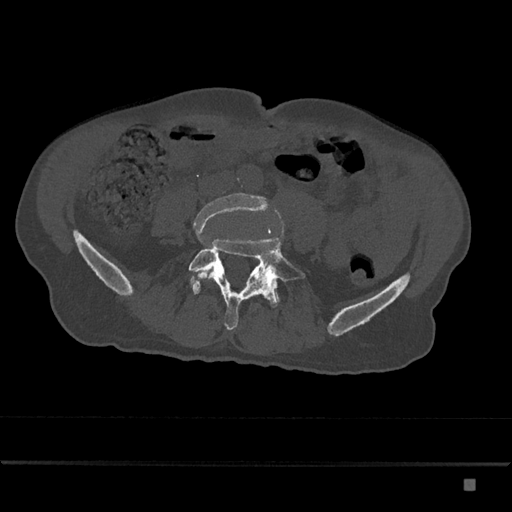
CT including the spine, one axial slice. Position 293 of 797 along the scan axis. 120 kVp. Bone window (W 1800 / L 400 HU). 0.5 mm slice thickness. 512 × 512 image matrix, field of view 390 × 390 mm. Patient: male, 72 years. From the clinical record (not read from this slice): primary cancer: prostate.
Outlined on this slice (semi-automatically segmented with operator editing):
- L4 vertebra: bounding box (x1, y1, x2, y2) in pixels: (193, 193, 268, 280)
- L5 vertebra: (189, 237, 305, 330)